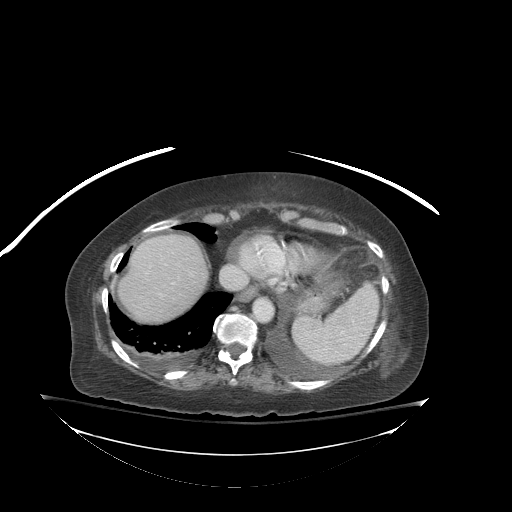
Contrast-enhanced abdominal CT (liver protocol), one axial slice; slice 73 of 81 in the series (ordered by position); soft-tissue window (W 400 / L 40 HU); 2.5 mm slice thickness; 512 × 512 image matrix, field of view 500 × 500 mm. From the clinical record (not read from this slice): diagnosis: hepatocellular carcinoma (patient treated with transarterial chemoembolisation; whether this scan precedes or follows treatment is not stated here); TNM stage (as recorded): Stage-I; Child-Pugh class: B.
Structures marked on this image (semi-automatically segmented with operator editing):
- abdominal aorta: box from (x=254, y=299) to (x=273, y=321) px
- liver parenchyma outside the tumour (the mass and vessels are separate outlines, so this box may not span the whole liver): (x=118, y=234)–(x=208, y=322)